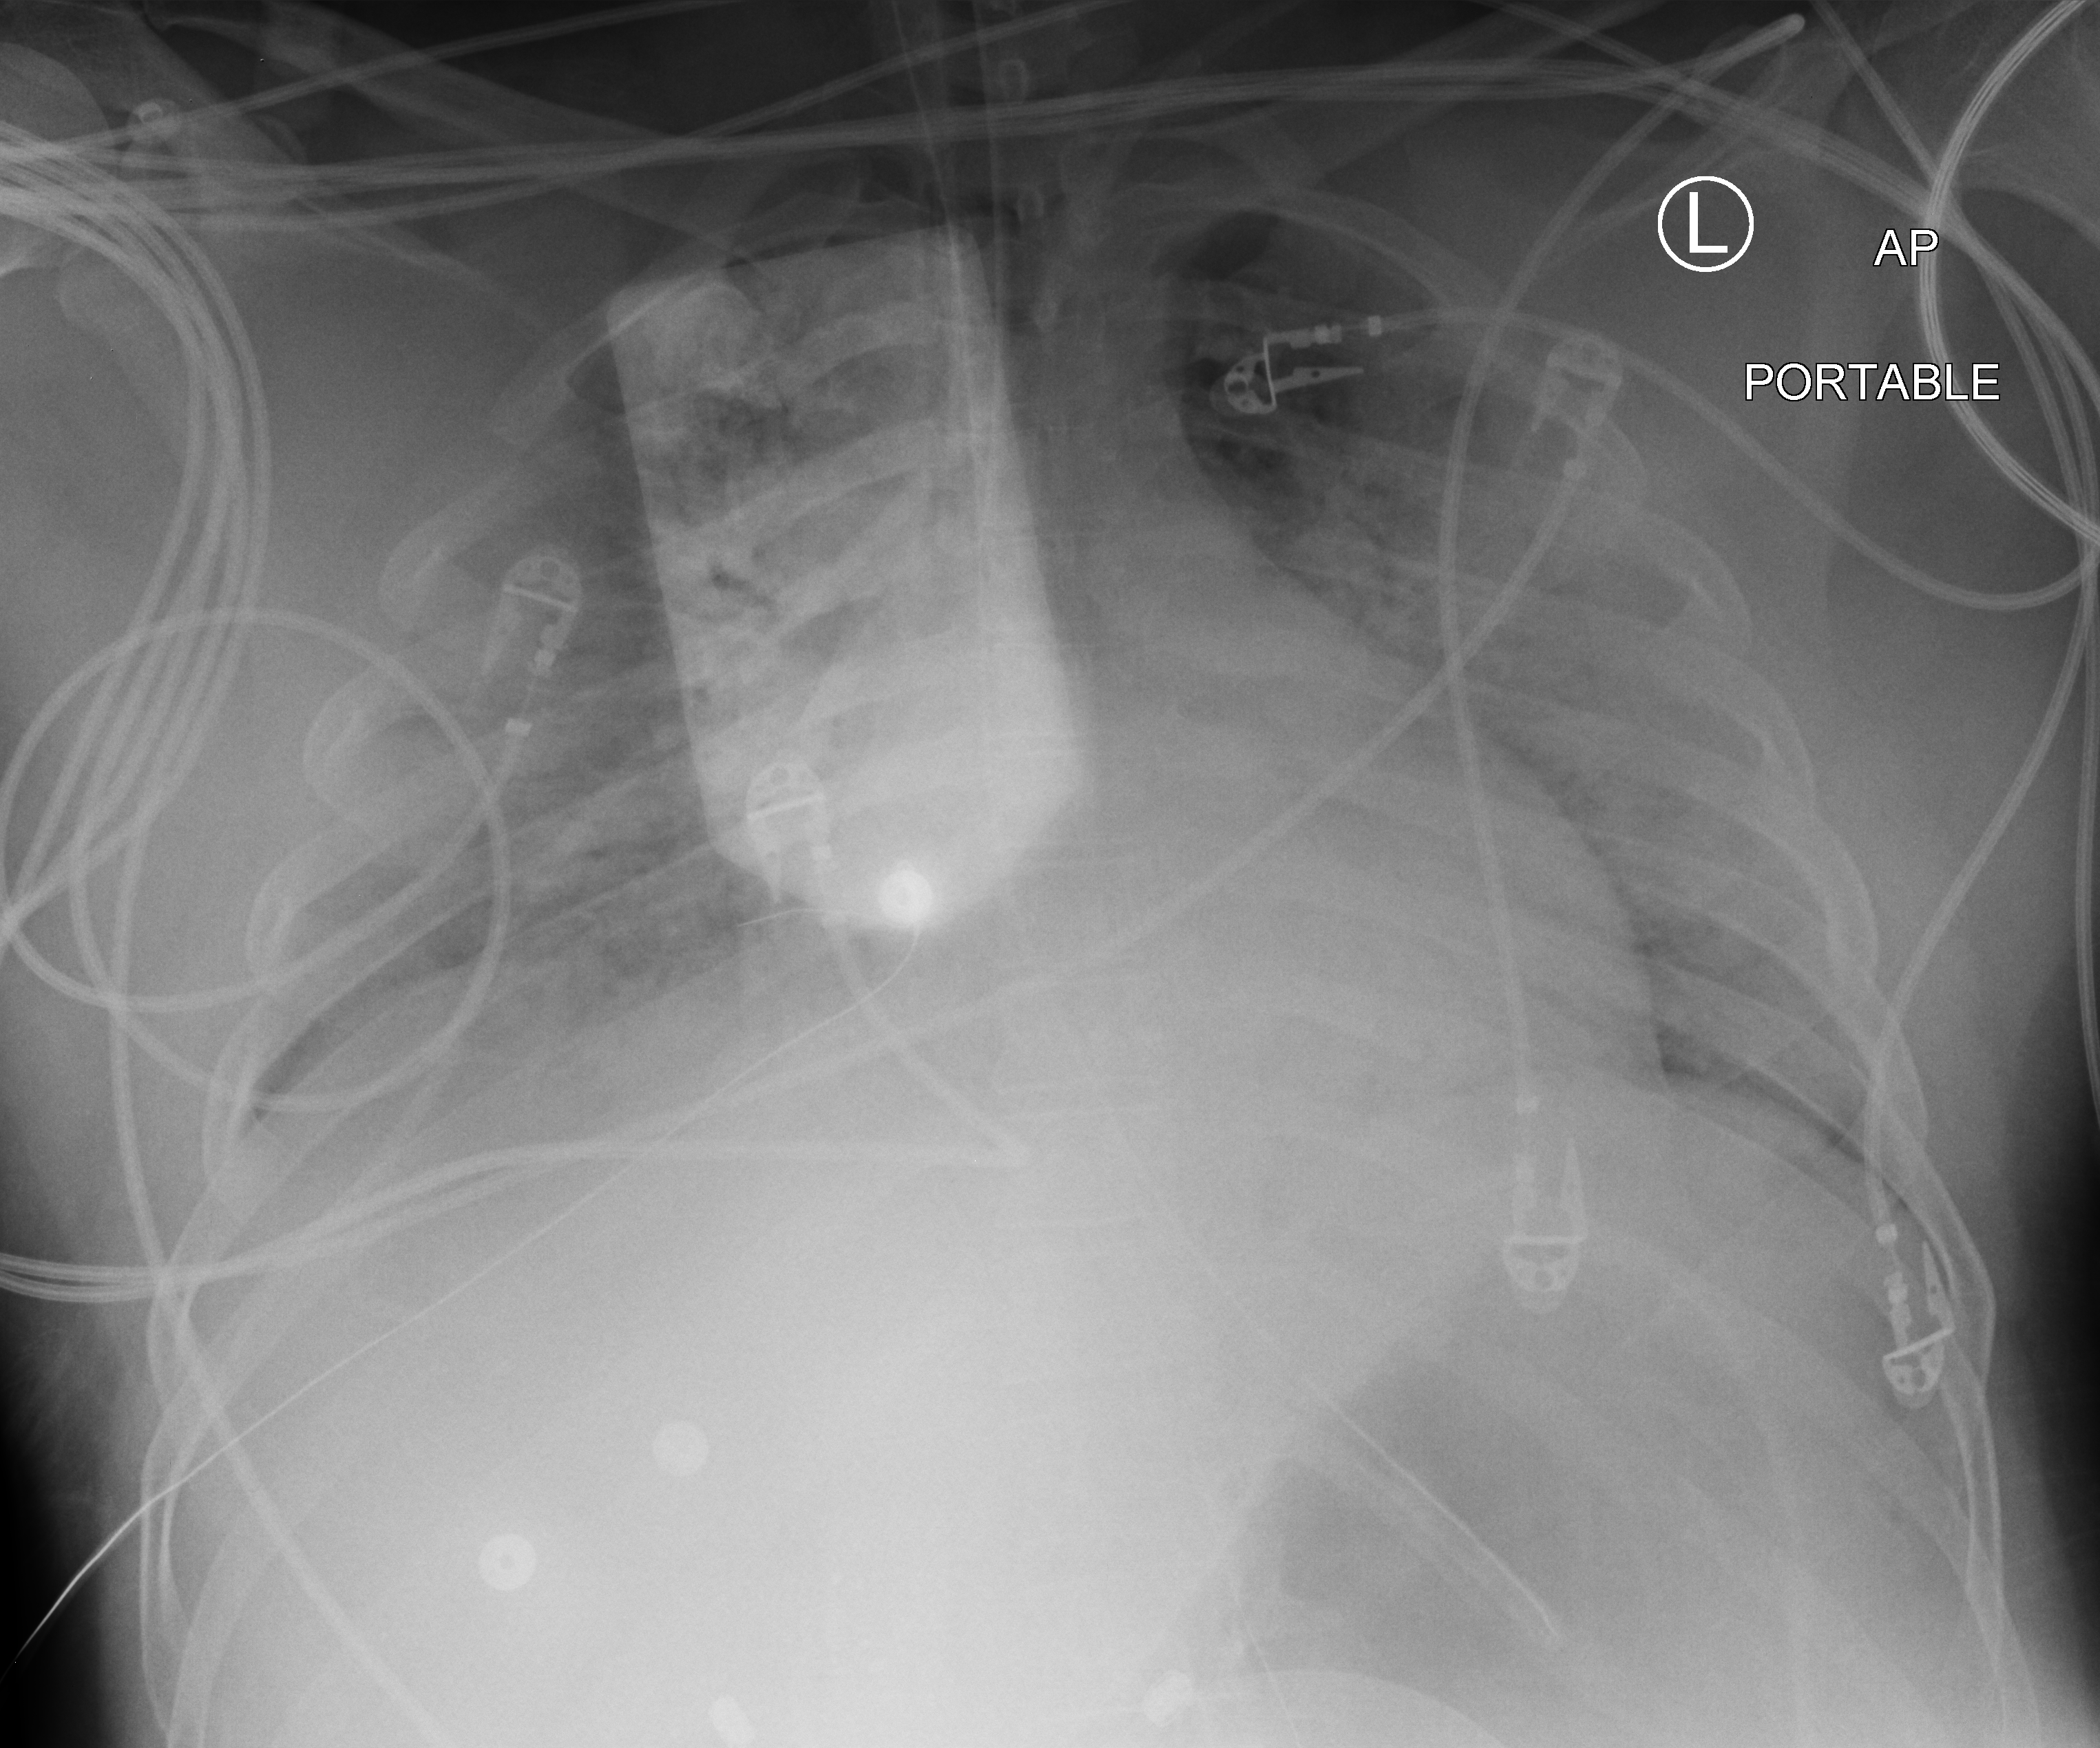
Bedside chest radiograph (computed radiography); anteroposterior (AP) projection. Adult patient hospitalised with COVID-19, age 18–59 years.
Admission-level facts for this patient (not findings on this image; timing relative to this image not recorded): smoking status (admission record): never; admitted to intensive care during this hospital stay: yes; mechanically ventilated during this hospital stay: yes.